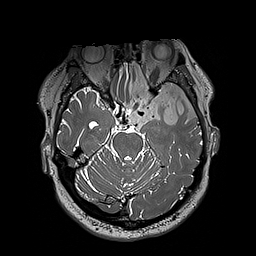
Brain MRI from a brain-tumour surgery series, one axial slice; slice 136 of 192 in the series (ordered by position); 1 mm slice thickness; 256 × 256 image matrix. Case-level facts recorded for this patient, not image findings: histopathology: Oligodendroglioma; WHO grade: 3; IDH mutation: yes; tumour location: Left Sylvian Fissure (Temporal).
Structures marked on this image (expert manual segmentation):
- tumour: box from (x=124, y=63) to (x=197, y=125) px